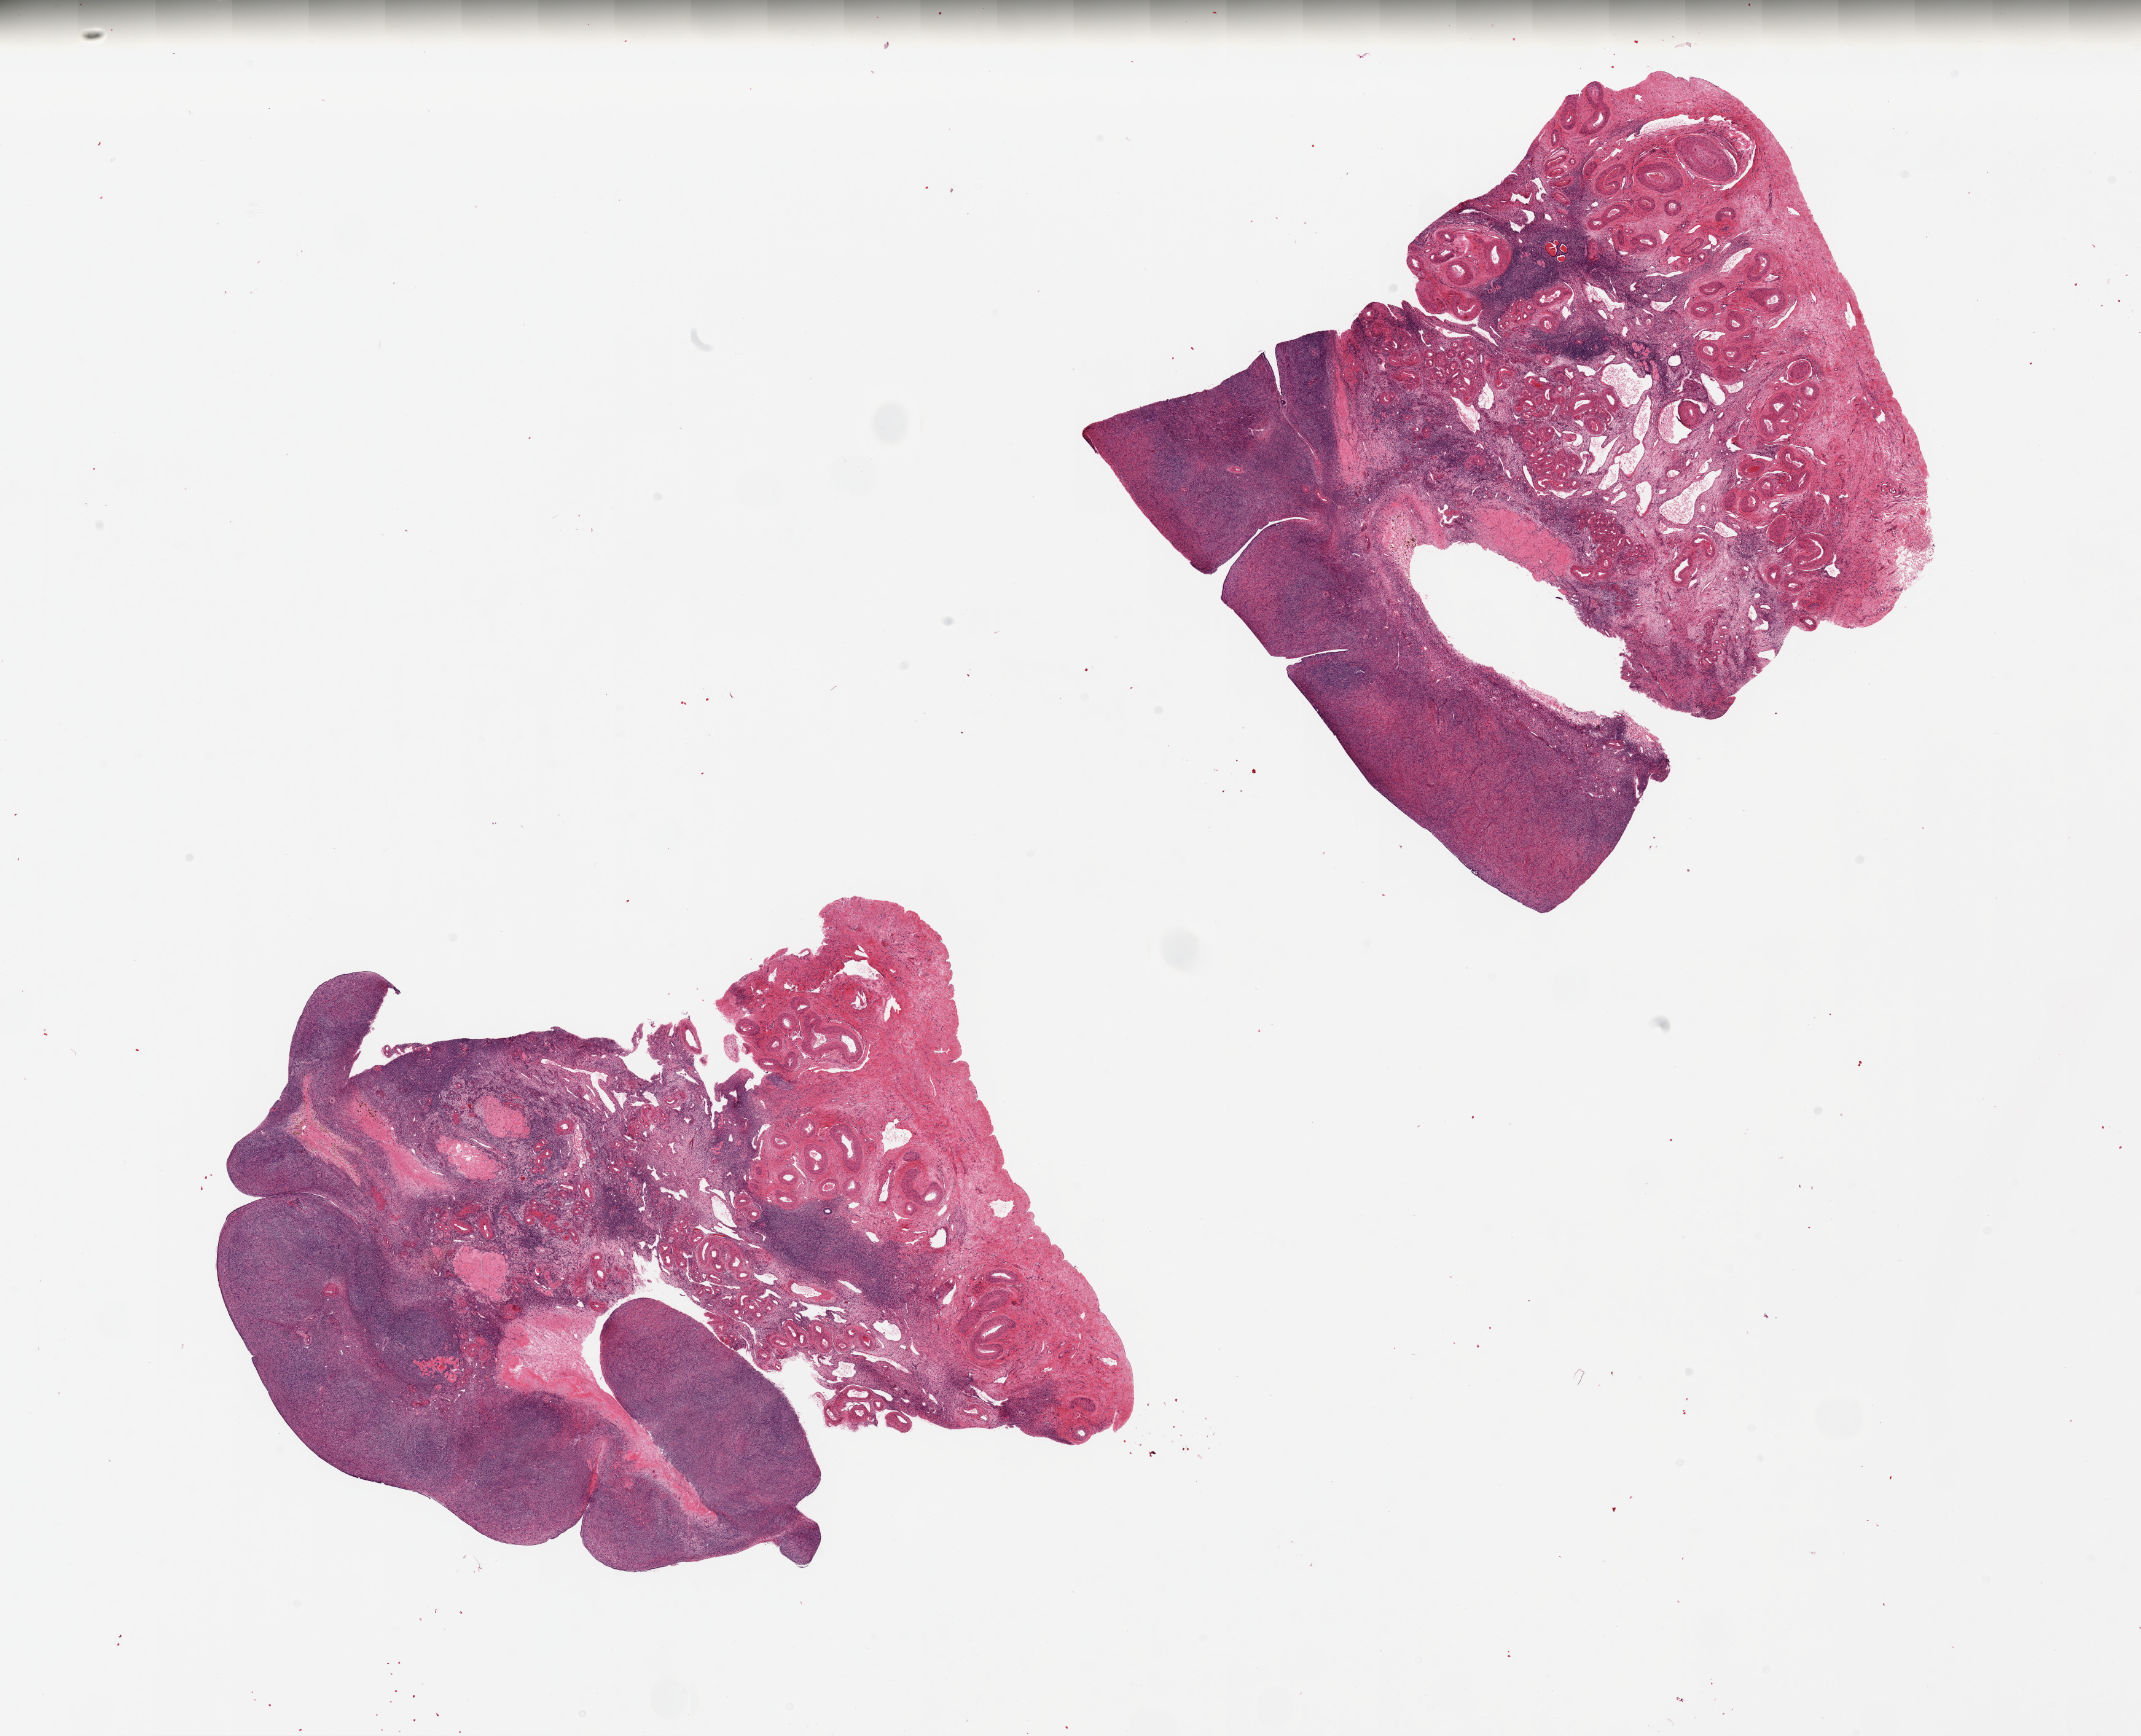
Whole-slide image, haematoxylin and eosin stain, brightfield, low-resolution overview of the scanned area, about 27.6 x 22.4 mm; PAXgene-fixed paraffin-embedded (PFPE) section; sampled site (target tissue): ovary; donor tissue sample. Female donor.
Review note (as recorded): 2 pieces, post menopausal involution; both are ~40-50% hilum.